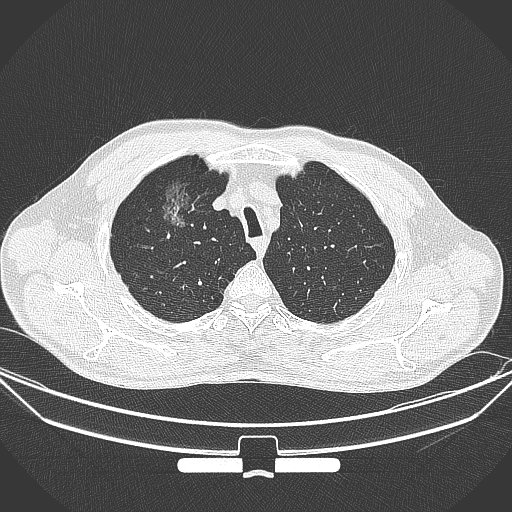
Chest CT, one axial slice; position 287 of 355 along the scan axis; lung window (W 1500 / L -600 HU); 1 mm slice thickness; 512 × 512 image matrix, field of view 399 × 399 mm. Male patient, age 67 years. Case-level facts recorded for this patient, not image findings: clinical TNM (as recorded): T1c N0 M0.
Structures marked on this image (rectangle marked by the reading radiologist):
- lung tumour (recorded histology: adenocarcinoma): bounding box [x1, y1, x2, y2] px = [152, 176, 194, 227]